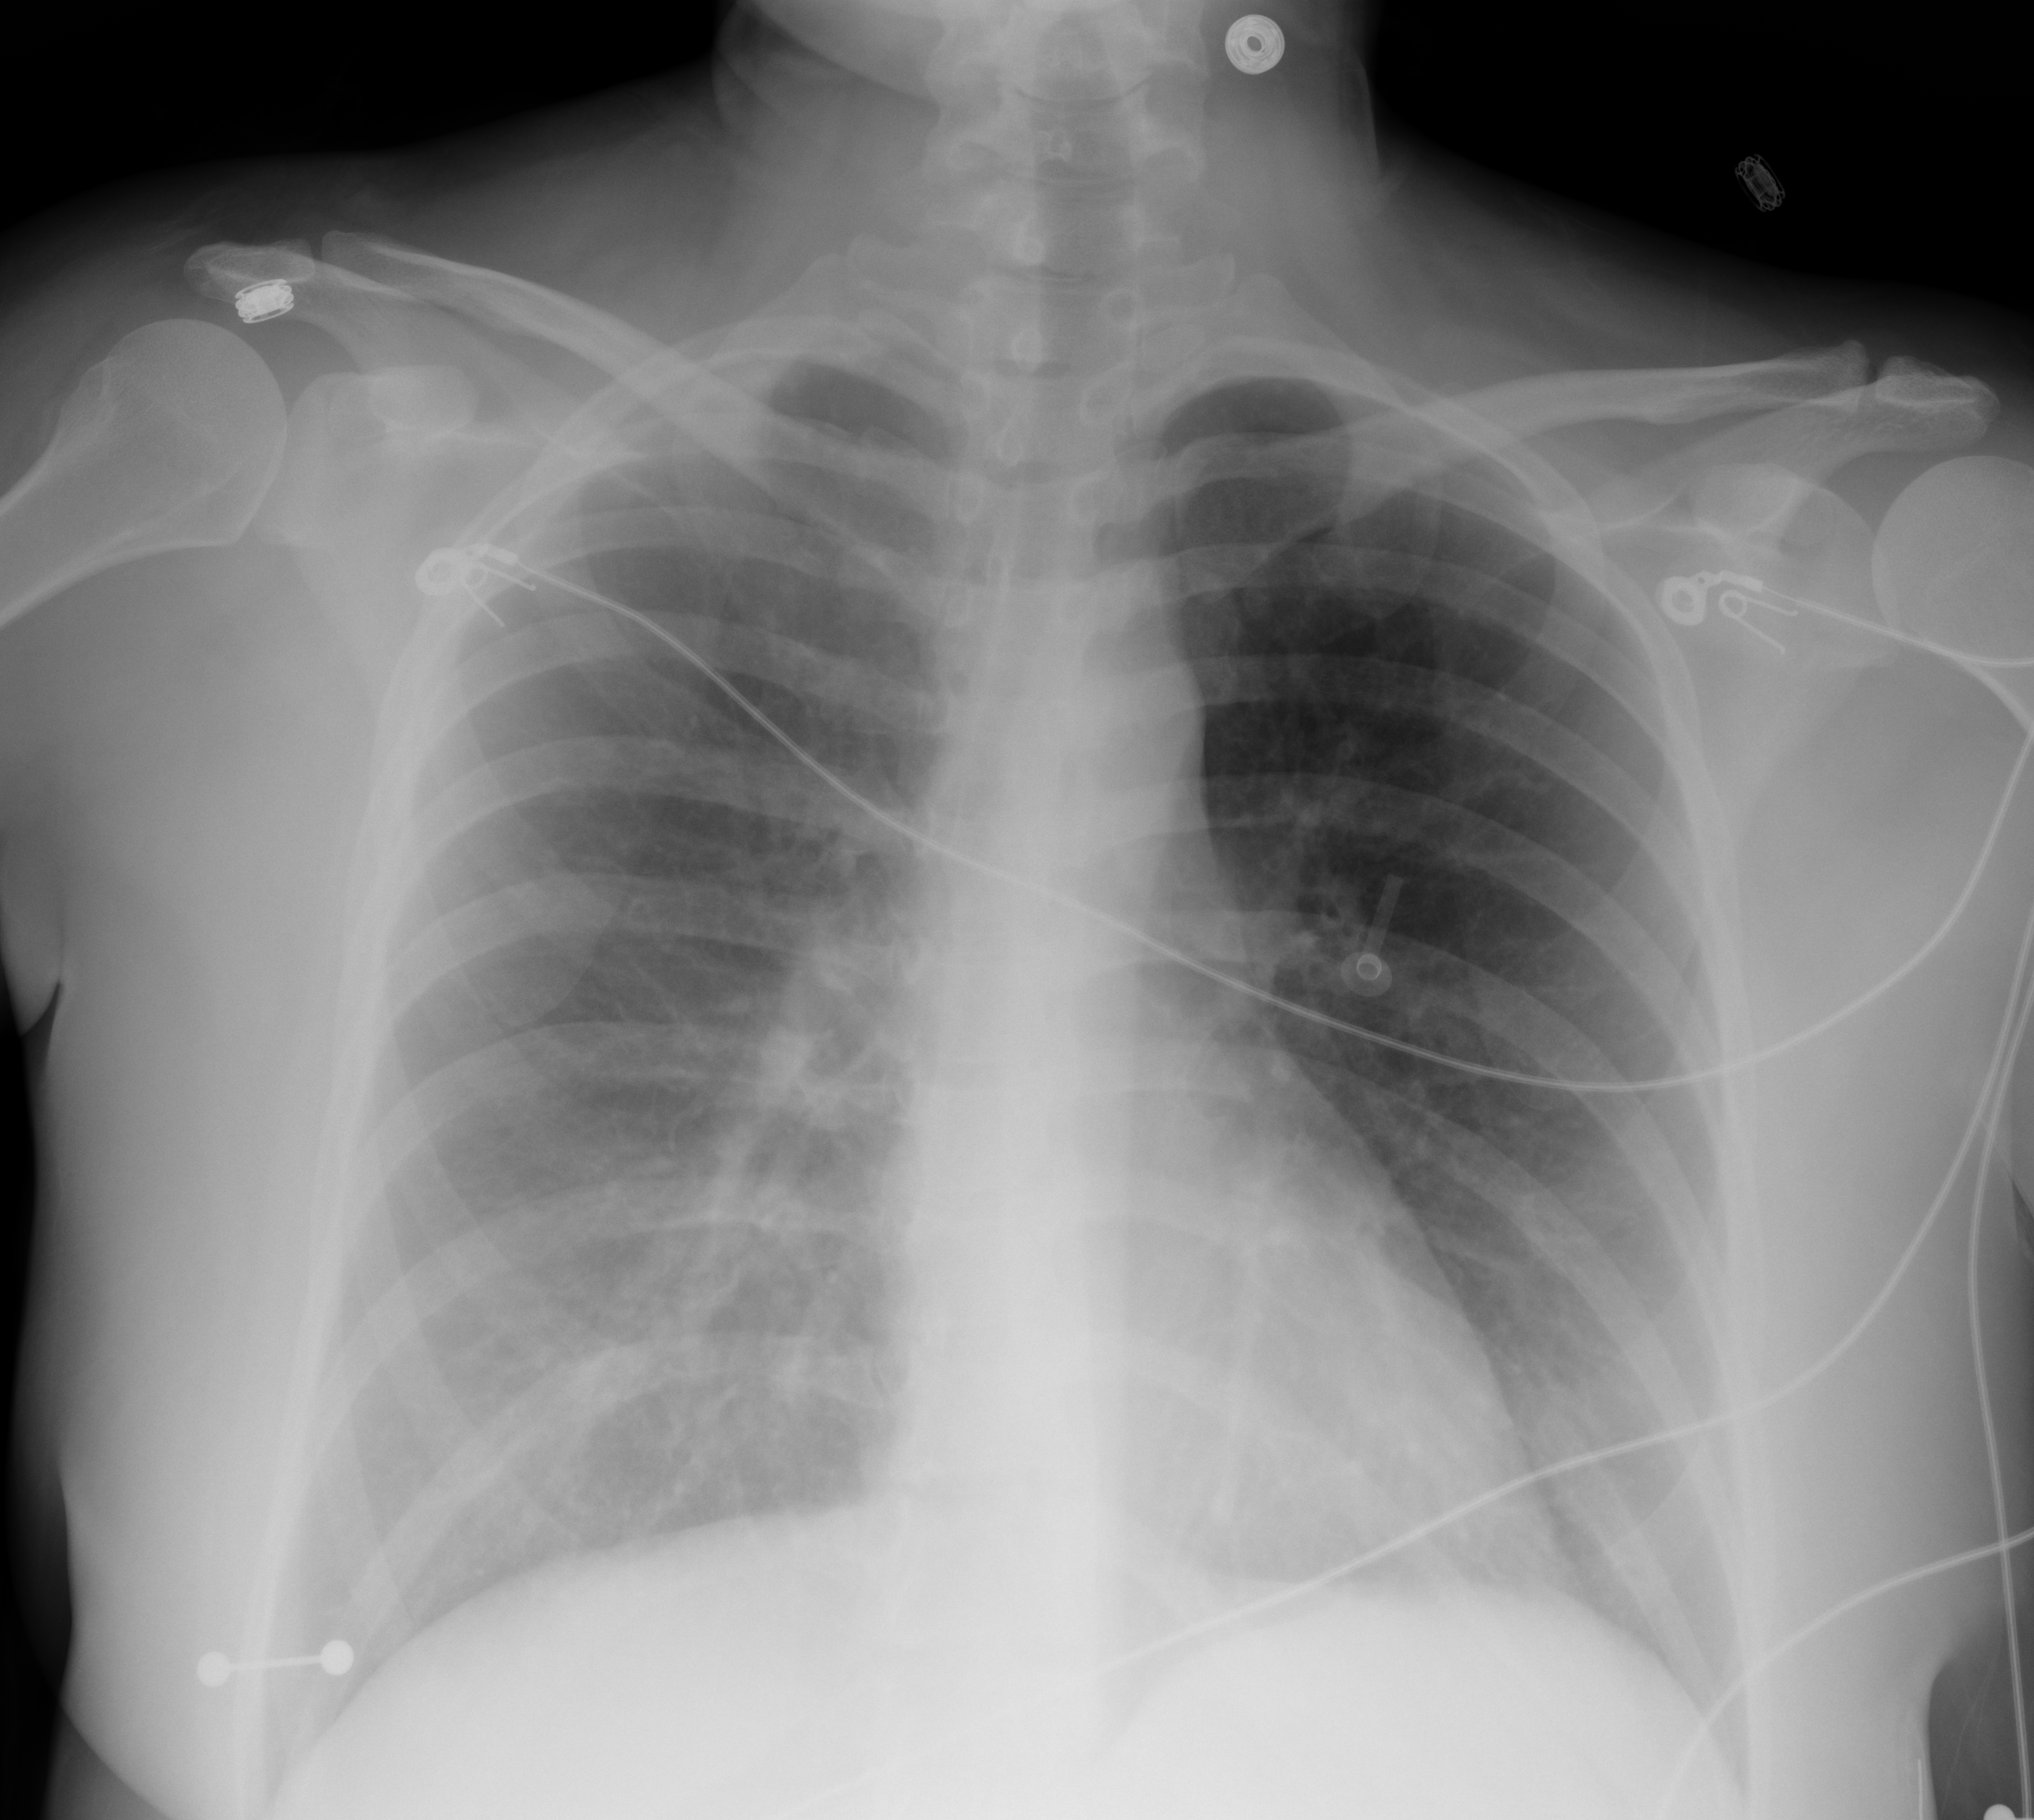
Portable chest radiograph, AP projection. Female patient, age 38 years; imaged 0 days after the COVID-19 diagnosis.
Key findings recorded by the radiologist: Subtle hazy opacities in the bilateral lung bases.